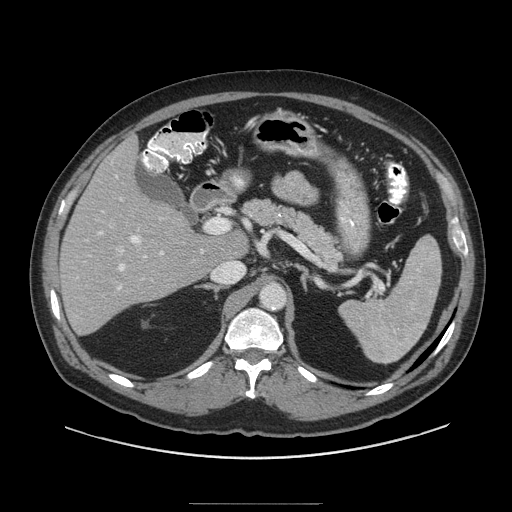
Contrast-enhanced abdominal CT (liver protocol), one axial slice. Position 56 of 91 along the scan axis. Reconstruction kernel STANDARD. 140 kVp. Soft-tissue window (W 400 / L 40 HU). 2.5 mm slice thickness. 512 × 512 image matrix, field of view 440 × 440 mm. From the clinical record (not read from this slice): diagnosis: hepatocellular carcinoma (patient treated with transarterial chemoembolisation; whether this scan precedes or follows treatment is not stated here); TNM stage (as recorded): Stage-I; Child-Pugh class: A.
Structures marked on this image (semi-automatic segmentation, software-assisted and operator-edited):
- liver parenchyma outside the tumour (the mass and vessels are separate outlines, so this box may not span the whole liver): bounding box (x1, y1, x2, y2) in pixels: (58, 136, 230, 334)
- liver vessels: (98, 175, 203, 290)